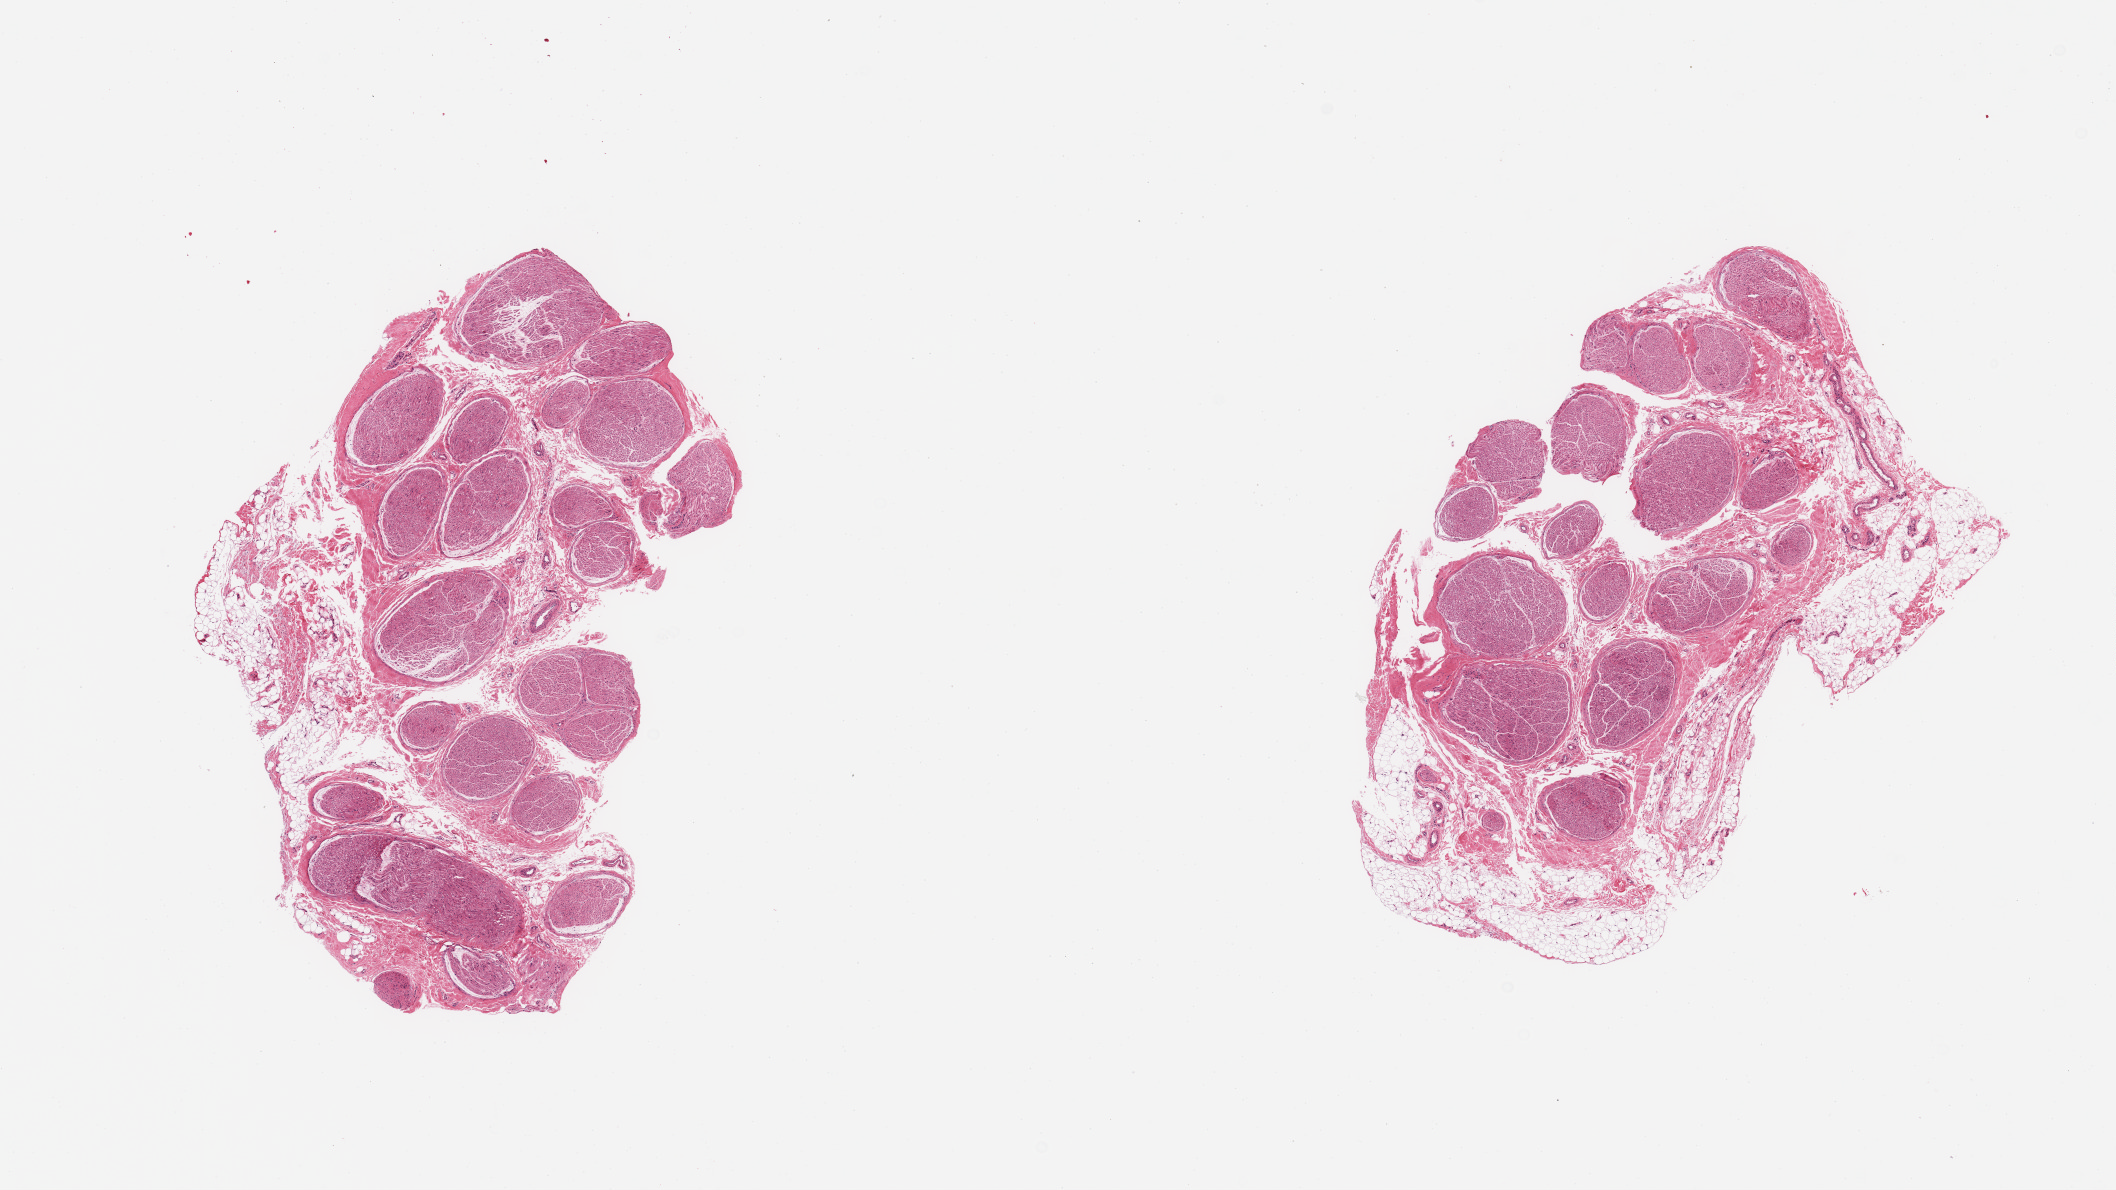
Digitized haematoxylin and eosin-stained section — low-resolution overview of the scanned area, about 16.7 x 9.4 mm (slide scanned at 20x). PAXgene-fixed paraffin-embedded (PFPE) section. Sampled site (target tissue): tibial nerve. Donor tissue sample.
Pathologist's review note for this sample: 2 pieces; 20% external and internal fat content.